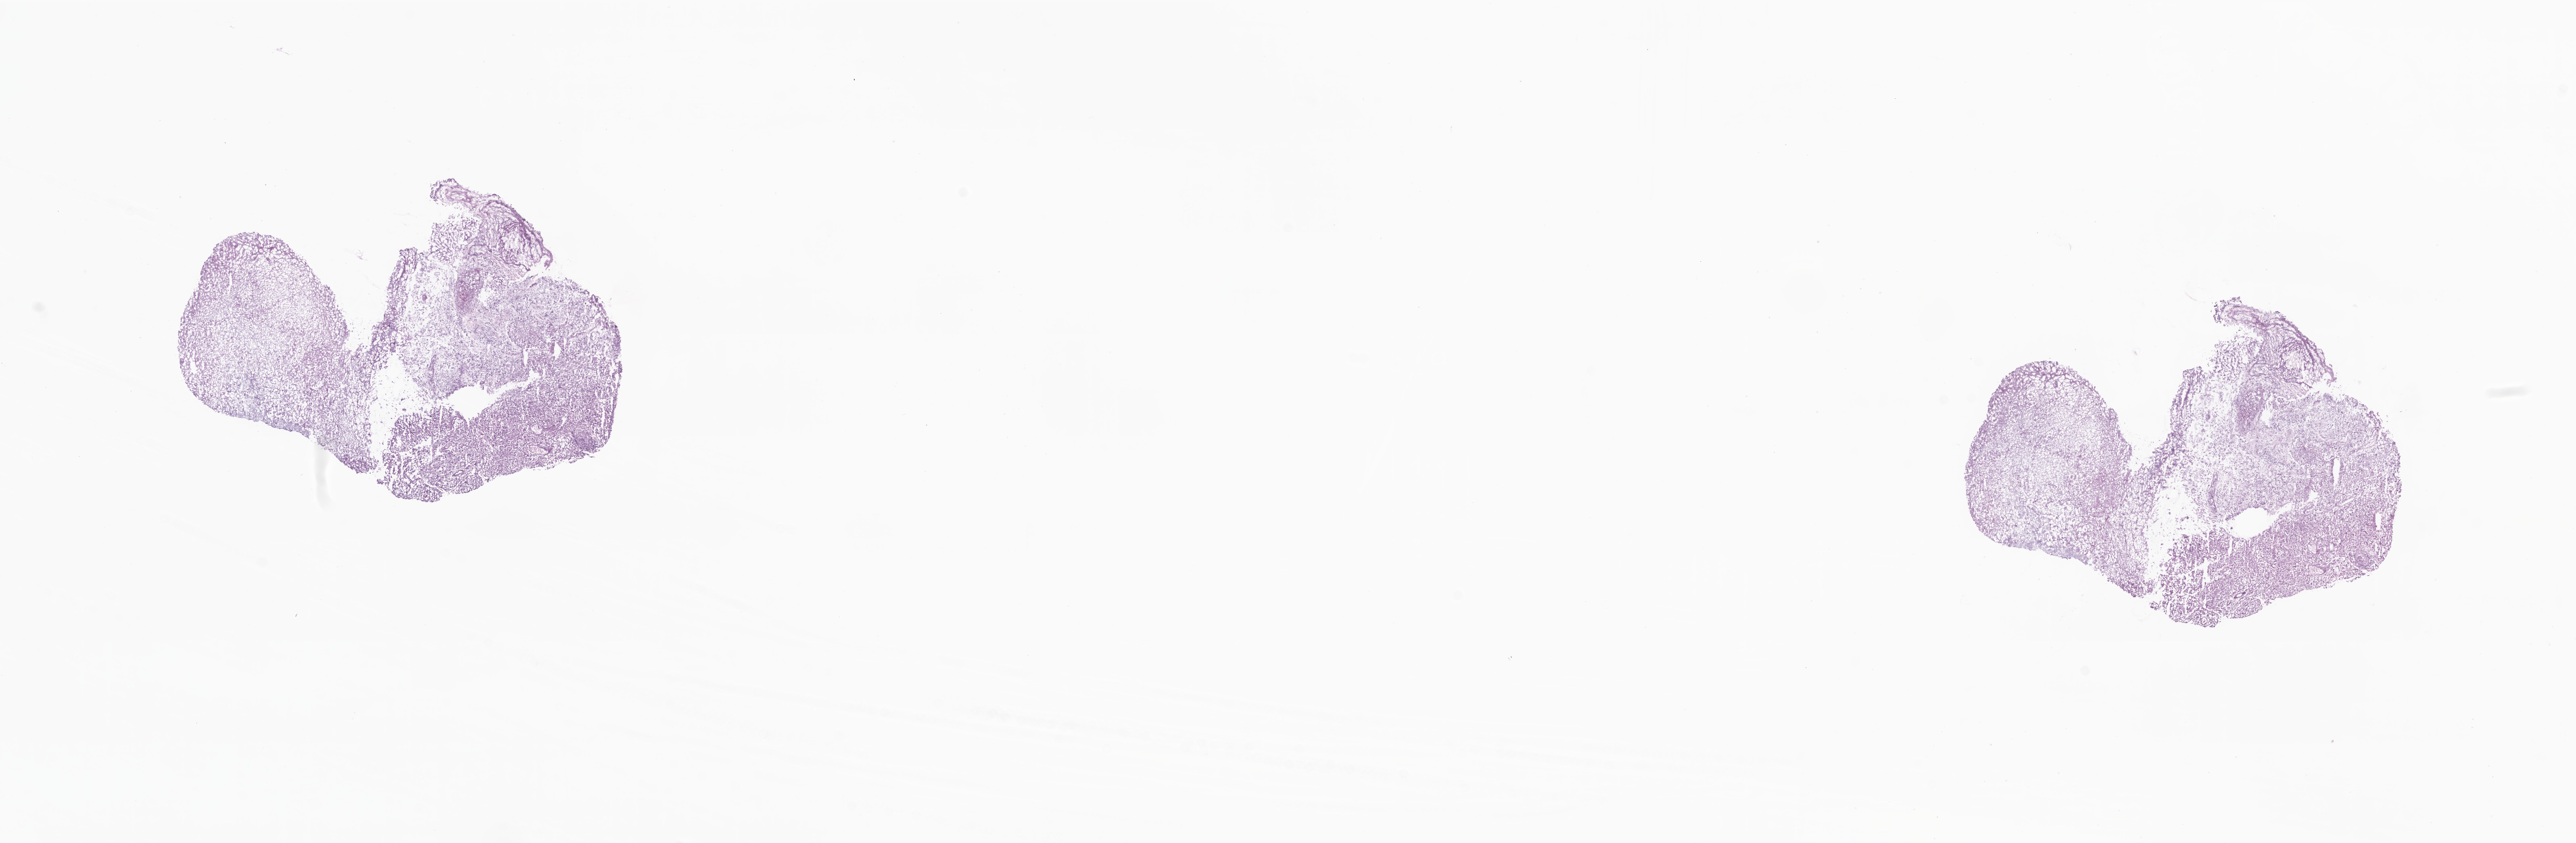
Digitized hematoxylin and eosin (H&E)-stained section, whole scanned area (about 26.9 x 8.8 mm) shown as a low-resolution overview; frozen section (tissue freezing medium); primary tumor; anatomic site: brain. Patient: female, age at initial diagnosis 69 years. Composition of this section per pathologist review: tumor cells 44%, tumor nuclei 92%, stromal cells 7%, necrosis 45%, normal cells 4%. Inflammatory infiltration, as recorded: lymphocyte infiltration 0%, monocyte infiltration 0%, neutrophil infiltration 0%.
* histologic diagnosis: Glioblastoma, NOS